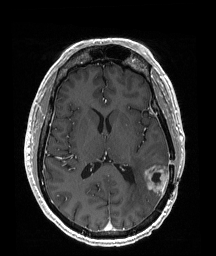
Brain MRI from a brain-tumour surgery series, one axial slice. Position 89 of 192 along the scan axis. T1-weighted post-contrast. 216 × 256 image matrix. Case-level facts recorded for this patient, not image findings: histopathology: Glioblastoma; WHO grade: 4; IDH mutation: no; tumour location: Left Temporoparietal.
Outlined on this slice (manually delineated by an expert):
- tumour: bounding box <144,166,170,197> (left, top, right, bottom; pixels)